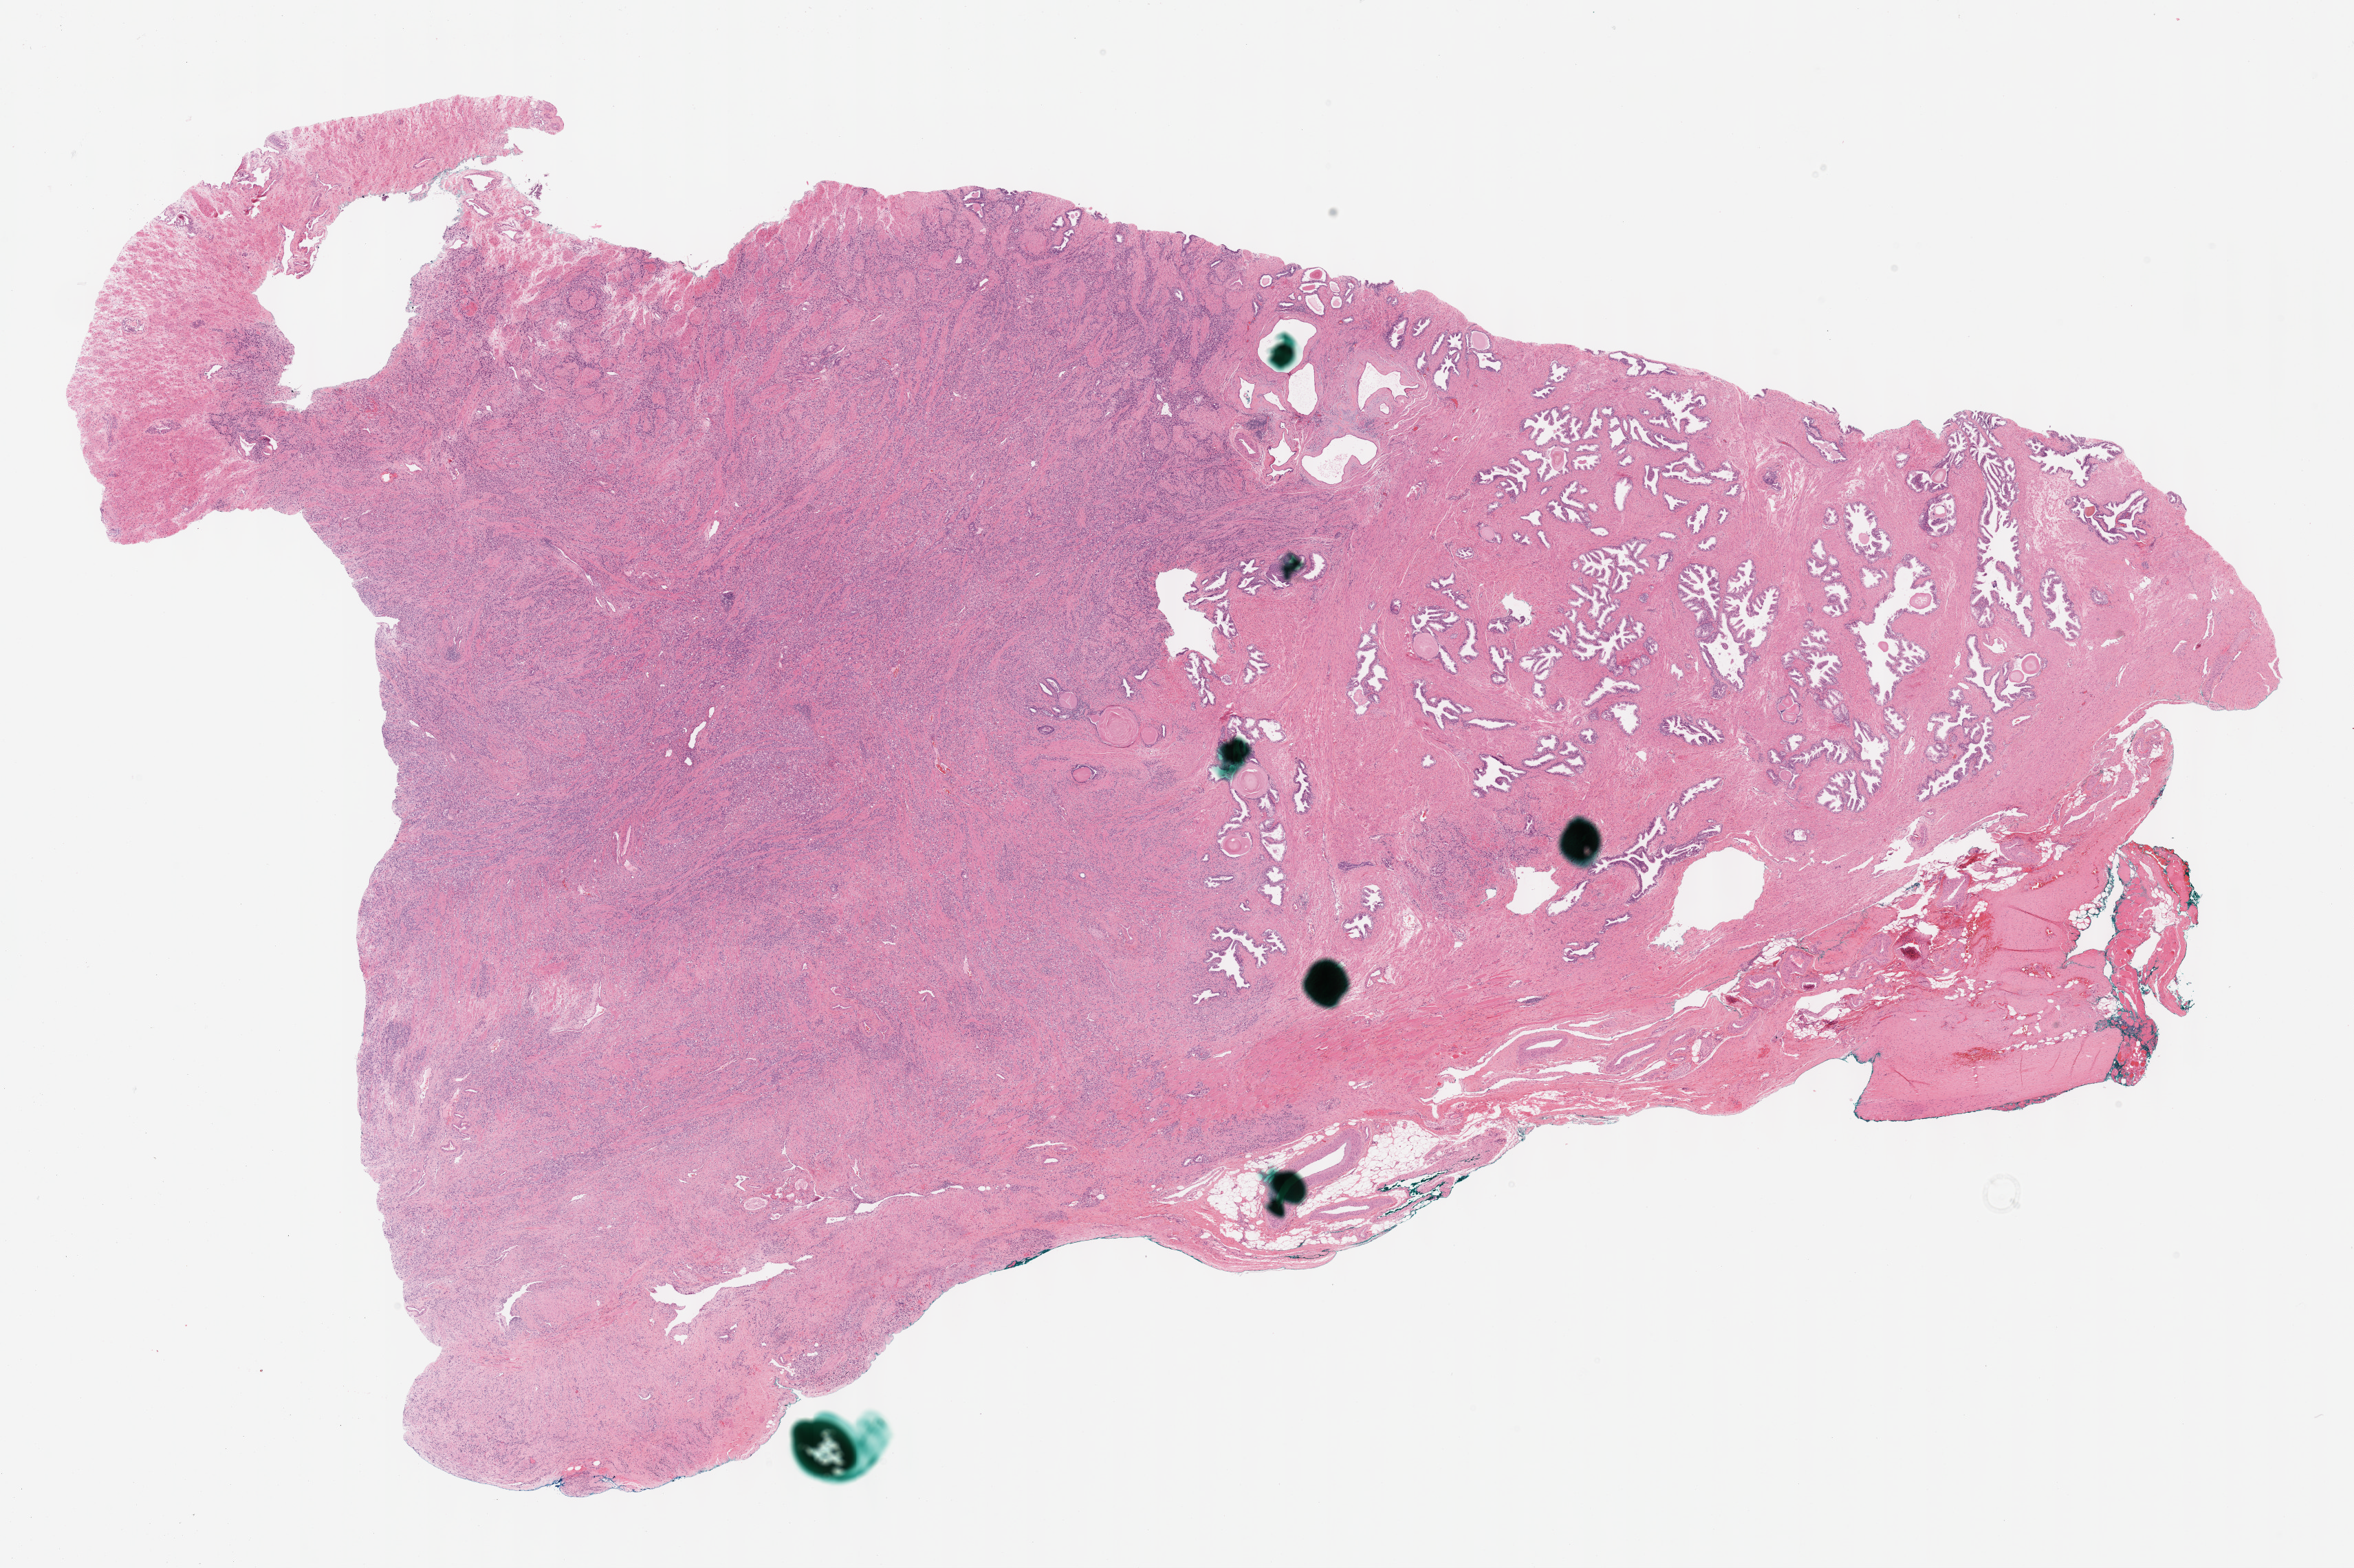
H&E-stained whole-slide image — whole scanned area (about 27.7 x 18.4 mm, from a 40x scan) shown as a low-resolution overview, formalin-fixed paraffin-embedded (FFPE) diagnostic section, sample: primary tumour, prostate. Male, age 60 years at initial diagnosis. Gleason score: 9 (5+4).
* laterality: bilateral
* histologic diagnosis: Adenocarcinoma, NOS (prostate gland)
* lymph nodes positive (case pathology): 0 of 15 examined